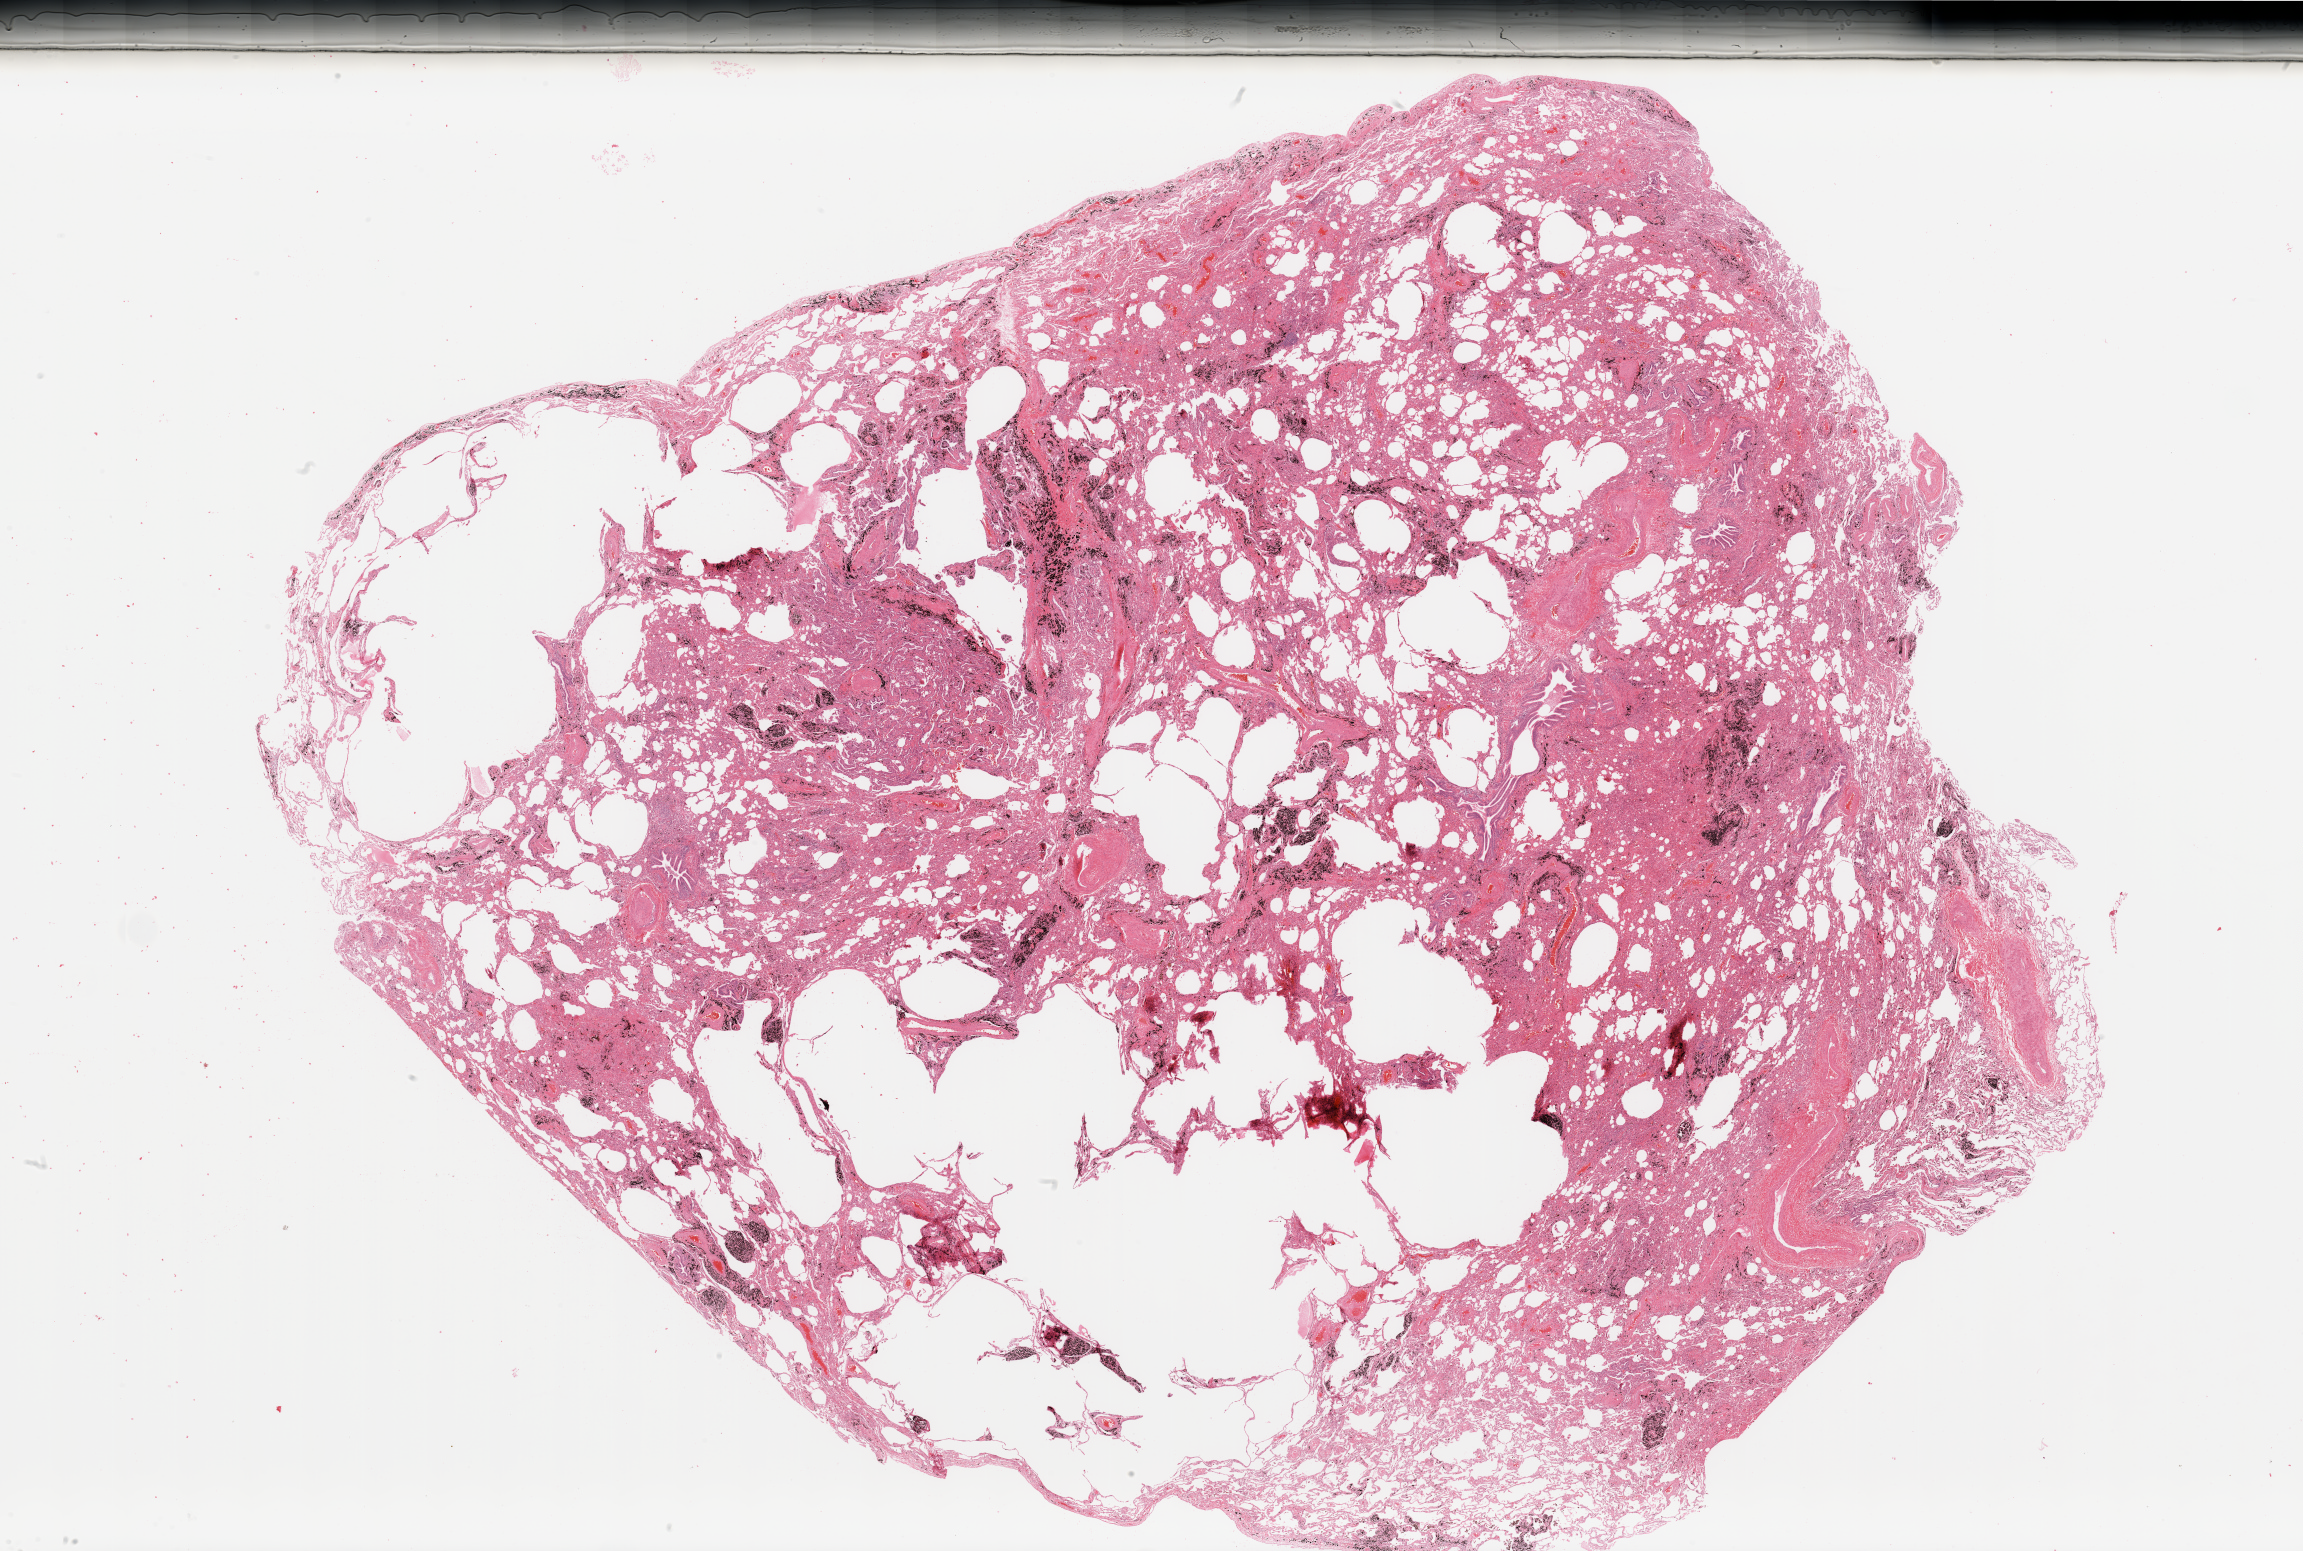
Digitized H&E tissue section (whole slide), shown as a low-resolution overview of the whole scanned area (about 36.4 x 24.5 mm), normal (non-tumour) tissue sample, lung. Male, 69 y/o.
This section: normal (non-tumour) tissue from the same patient. Patient diagnosis: Adenocarcinoma, NOS.